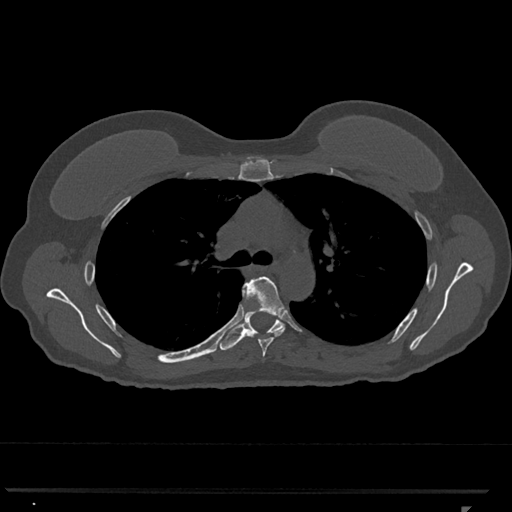
CT including the spine, one axial slice; position 786 of 793 along the scan axis; reconstruction kernel Br40s/3; bone window (W 1800 / L 400 HU); 0.5 mm slice thickness; 512 × 512 image matrix, field of view 380 × 380 mm. Patient: female, 62 years. From the clinical record (not read from this slice): primary cancer: renal.
Outlined on this slice (semi-automatically segmented with operator editing):
- T5 vertebra: bounding box (x1, y1, x2, y2) in pixels: (241, 276, 287, 357)
- T6 vertebra: (219, 282, 284, 350)